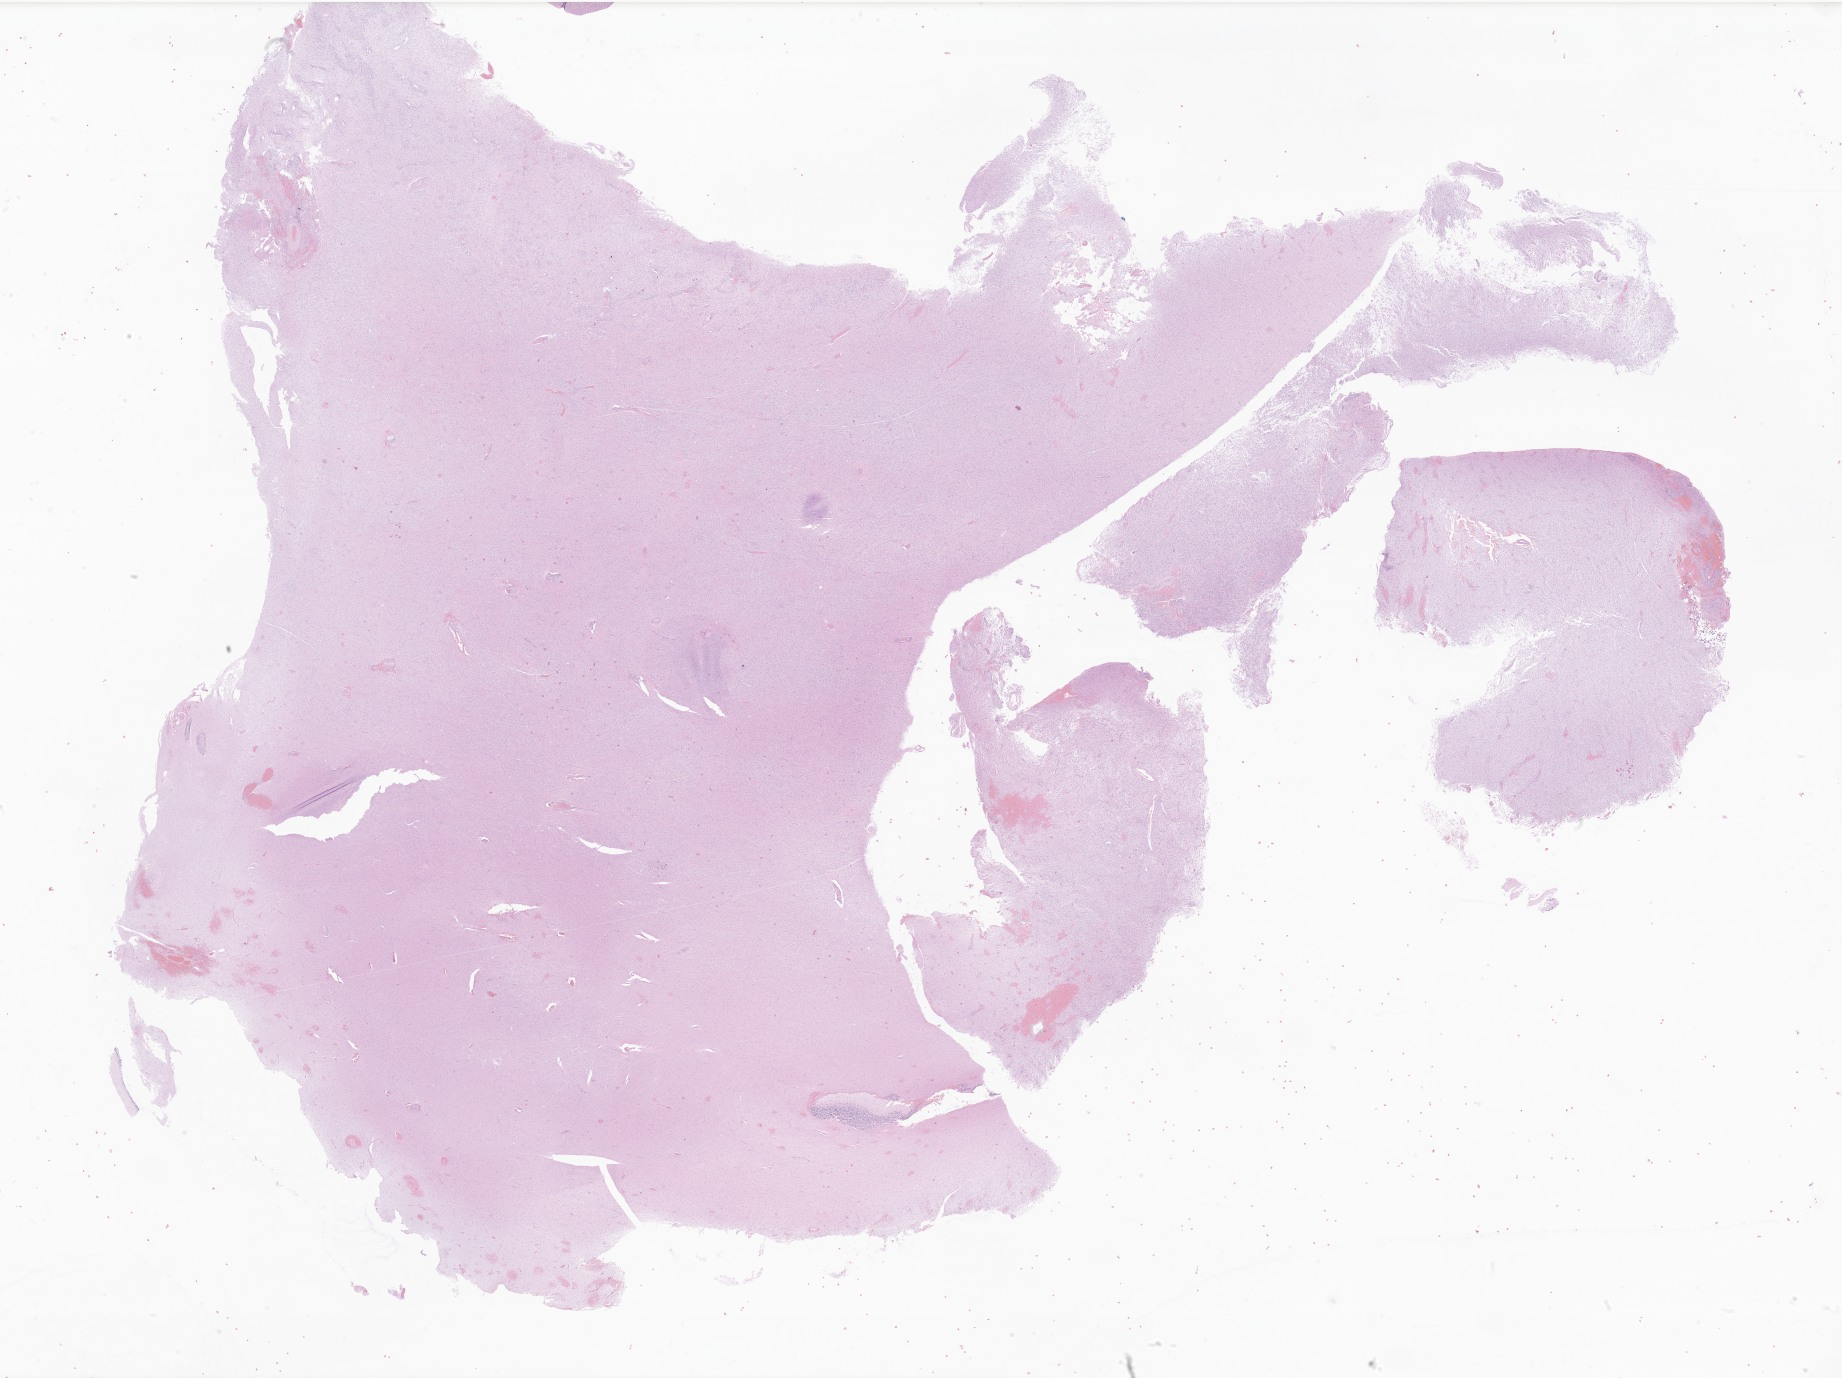
Whole-slide image, H&E stain of tumor tissue from the temporal lobe — whole scanned area (about 31.1 x 23.2 mm) shown as a low-resolution overview, FFPE section. Female patient, age 164 months (13 years 8 months).
Recorded diagnosis: Pilocytic astrocytoma.